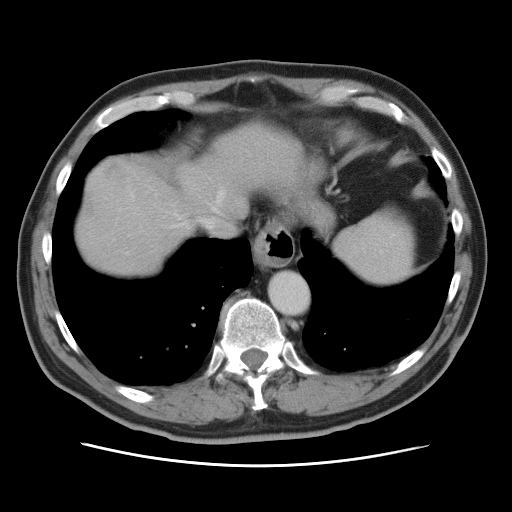
Contrast-enhanced abdominal CT, one axial slice; position 69 of 80 along the scan axis; 120 kVp; intravenous contrast given; soft-tissue window (W 400 / L 40 HU); 512 × 512 image matrix, field of view 370 × 370 mm. Male patient, age 69 years. Case-level facts recorded for this patient, not image findings: diagnosis: colorectal cancer liver metastases, imaged before liver resection; multiple liver metastases: no; largest metastasis: 5 cm.
Structures marked on this image (manually delineated by an expert):
- hepatic veins: bounding box <128,188,225,231> (left, top, right, bottom; pixels)
- liver: <75,120,297,276>
- planned liver remnant (the part of the liver to remain after resection): <75,120,296,276>
- liver metastasis: <103,166,122,175>